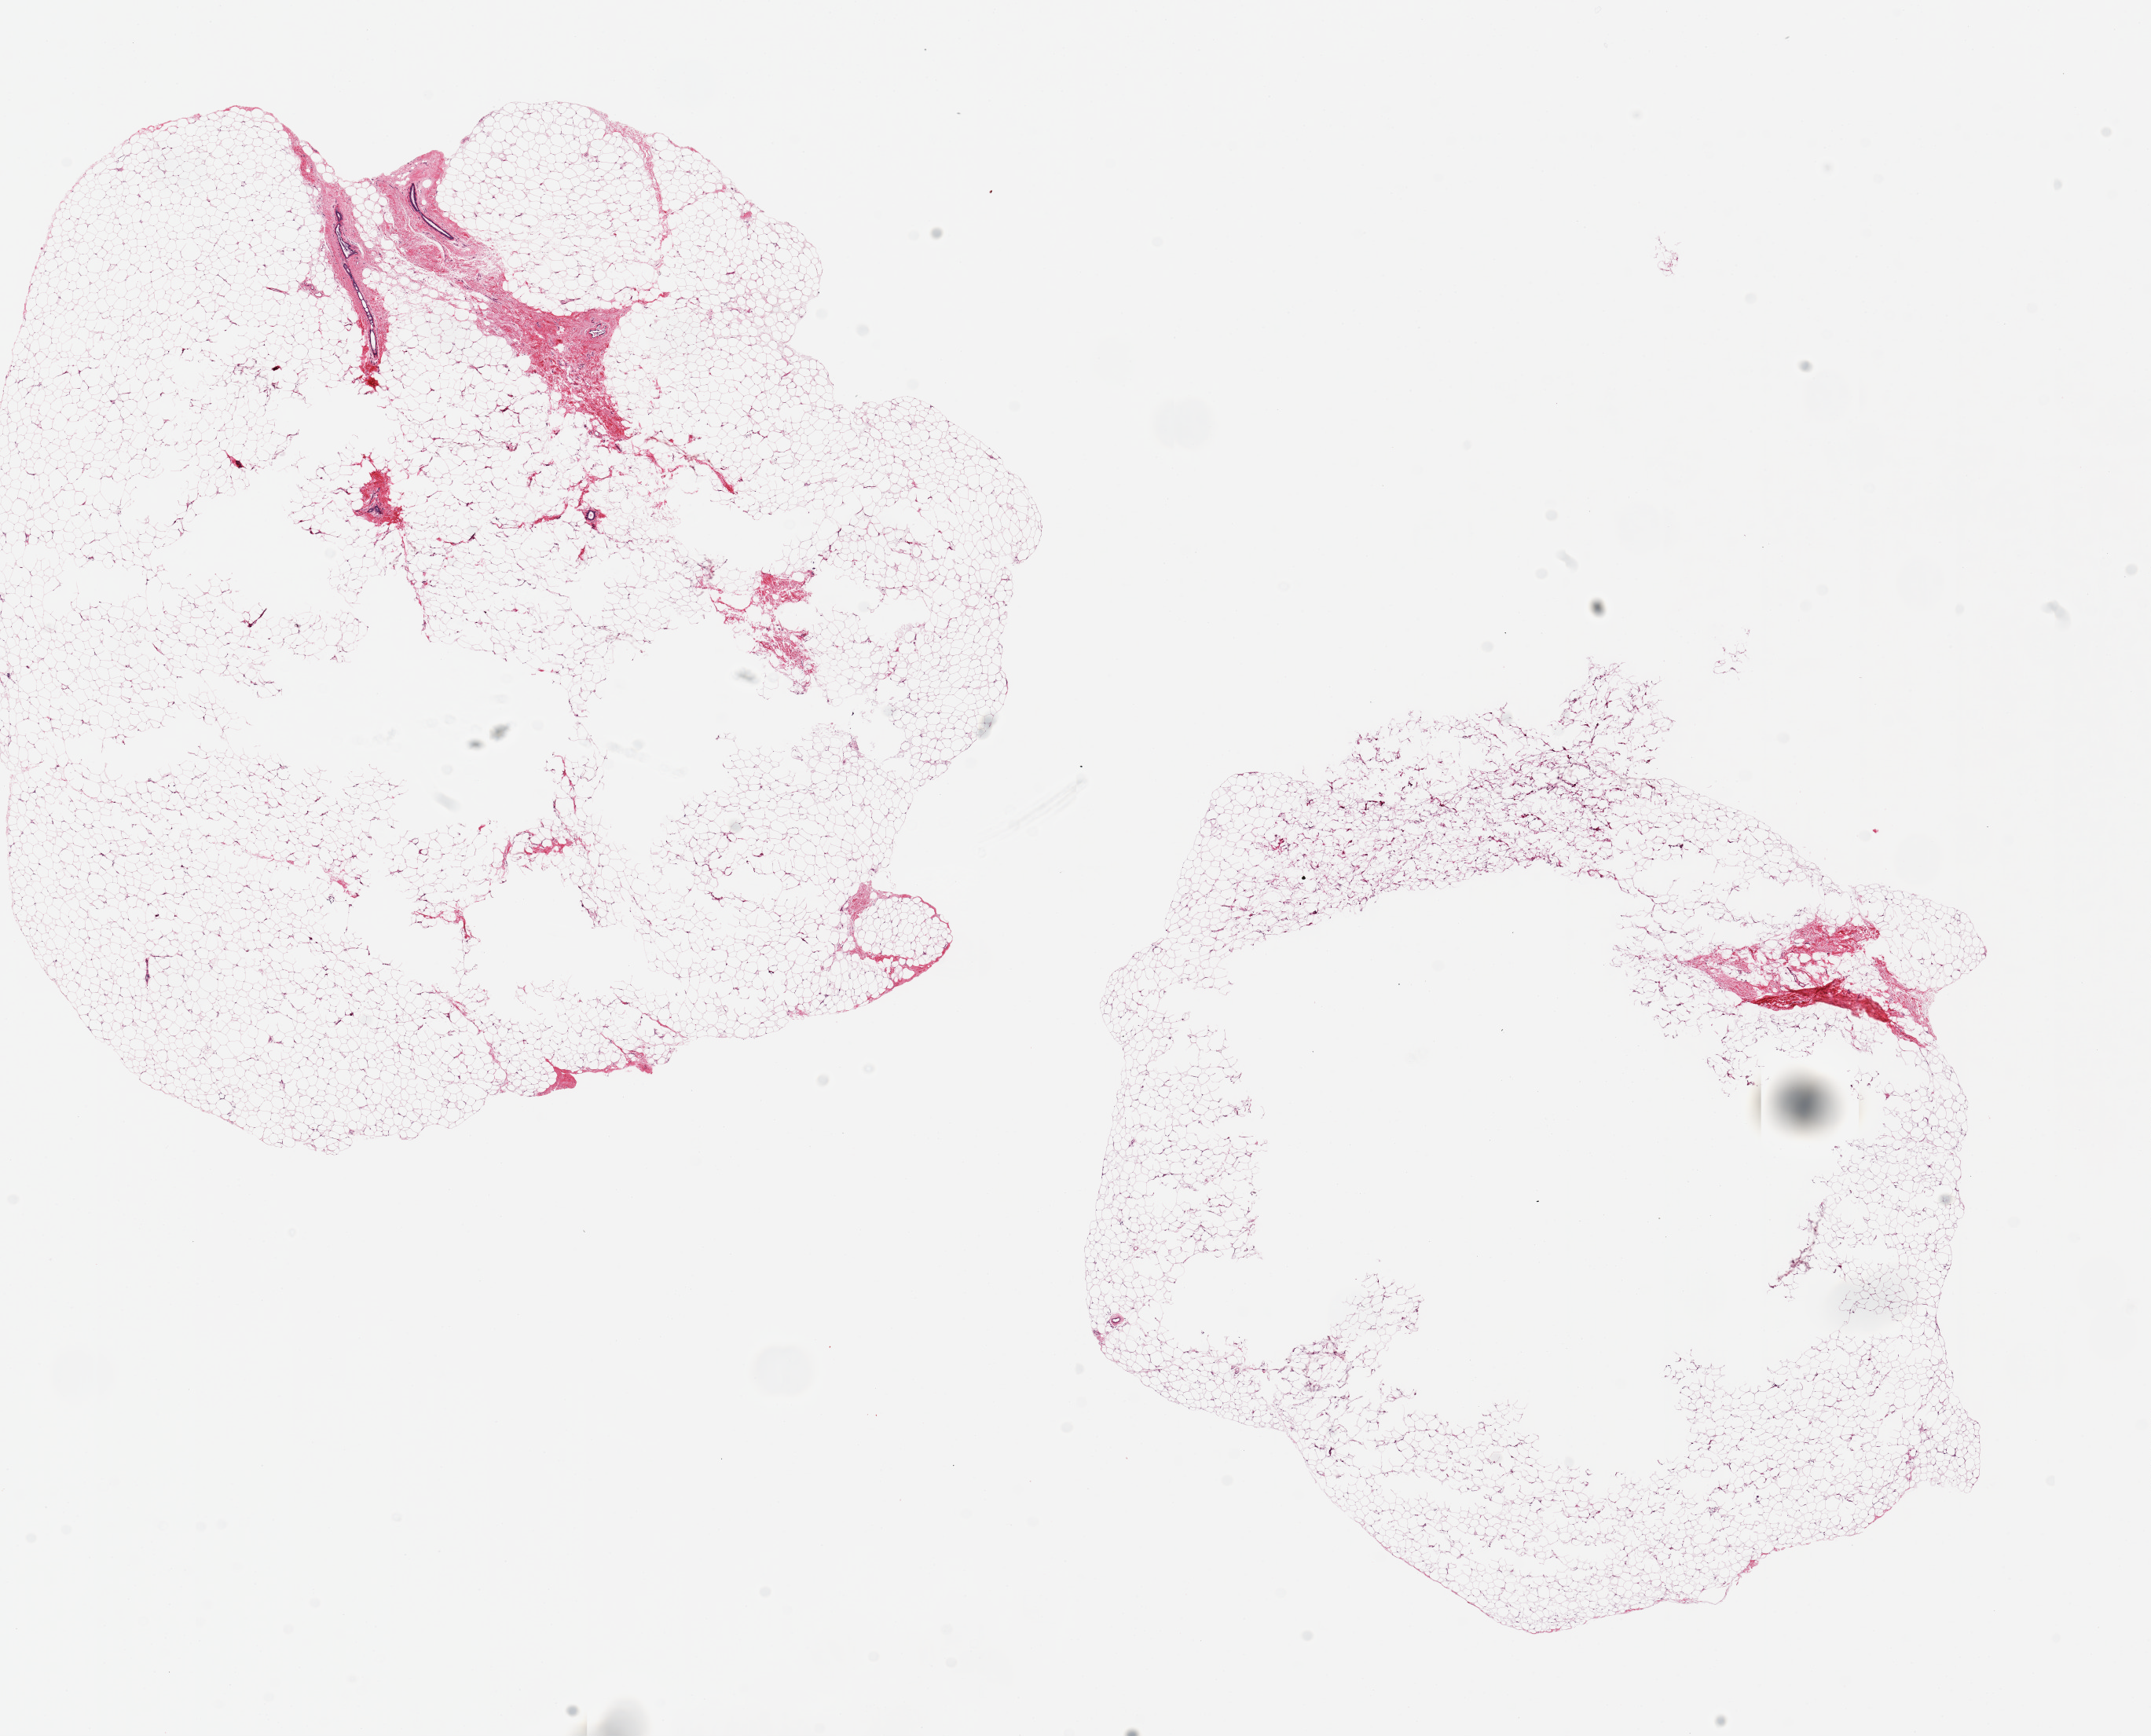
H&E whole-slide image, brightfield — whole scanned area (about 21.7 x 17.5 mm, acquisition: 20x scan) shown as a low-resolution overview. PAXgene-fixed, paraffin-embedded tissue. Section of breast (target tissue). Donor tissue sample. Donor: male.
Review note (as recorded): 2 pieces ~10x10mm; Essentially all fat; a few trace ductal units noted.